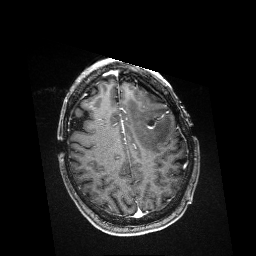
Brain MRI from a brain-tumour surgery series, one axial slice. Position 120 of 176 along the scan axis. T1-weighted post-contrast. 1 mm slice thickness. 256 × 256 image matrix, field of view 256 × 256 mm. Case-level facts recorded for this patient, not image findings: histopathology: Metastatic Melanoma; tumour location: Left Frontal.
Annotated regions visible in this slice (outlined manually by an expert reader):
- residual tumour: bounding box <147,125,155,129> (left, top, right, bottom; pixels)